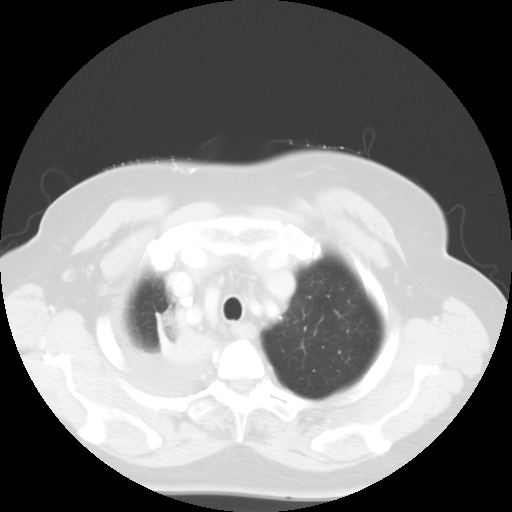
Chest CT, one axial slice. Position 46 of 52 along the scan axis. Reconstruction kernel STANDARD. Lung window (W 1500 / L -600 HU). 512 × 512 image matrix. Female patient, age 81 years. Case-level facts recorded for this patient, not image findings: clinical TNM (as recorded): T4 N3 M1b.
Outlined on this slice (bounding box drawn by a radiologist):
- lung tumour (recorded histology: adenocarcinoma): bounding box <147,309,219,371> (left, top, right, bottom; pixels)